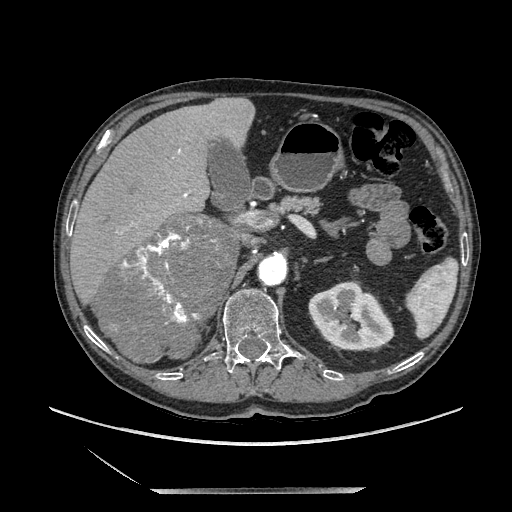
Contrast-enhanced abdominal CT, one axial slice. Position 126 of 243 along the scan axis. Soft-tissue window (W 400 / L 40 HU). 512 × 512 image matrix. Male patient. Case-level facts recorded for this patient, not image findings: diagnosis: adrenocortical carcinoma; tumour side: right adrenal; tumour size at pathology: 16 cm; Ki-67 index: 17 %; stage (as recorded): 3.
Outlined on this slice (semi-automatically segmented with operator editing):
- mass: box from (x=99, y=214) to (x=236, y=362) px